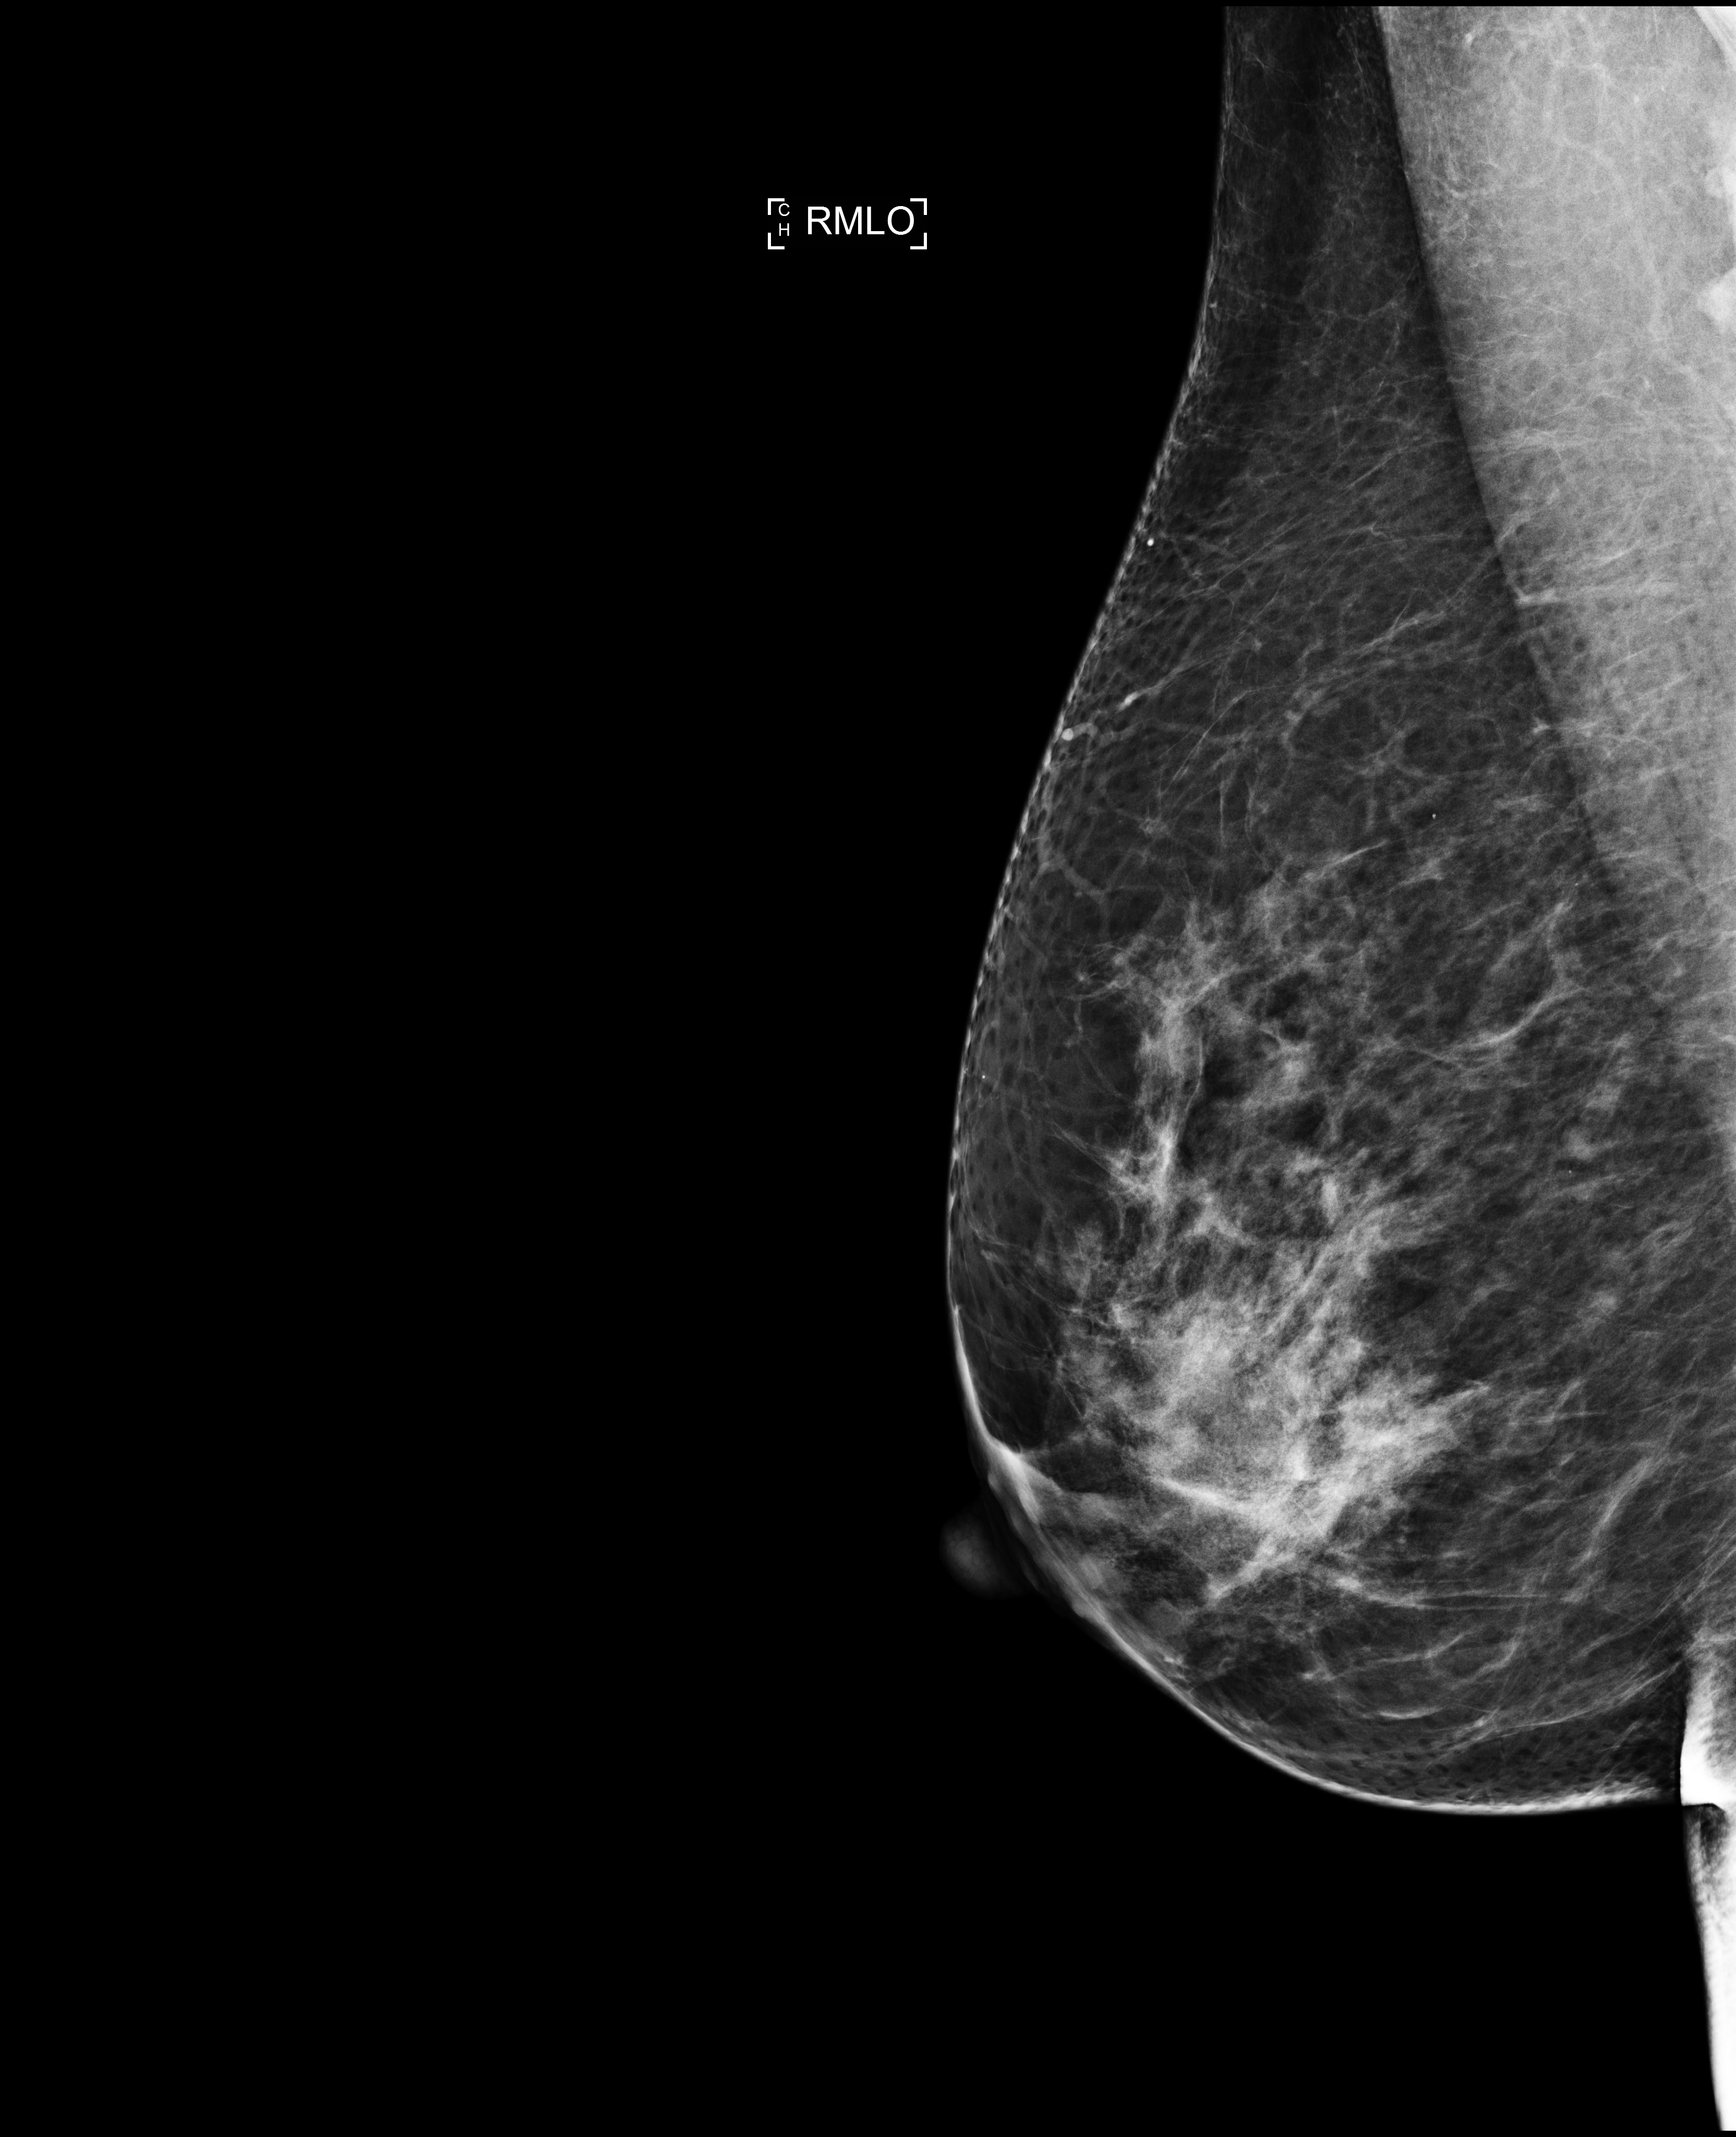
Full-field digital mammogram (FFDM); right breast; MLO view; annual screening mammography examination; compressed breast thickness 82 mm; system: Selenia Dimensions. Patient: female, 49 years.
- BI-RADS breast density category at the screening exam (both breasts, scale 1–4): 3
- final BI-RADS category for the screening round (tomosynthesis exam, both breasts): category 1
- recall: no recall after this screen